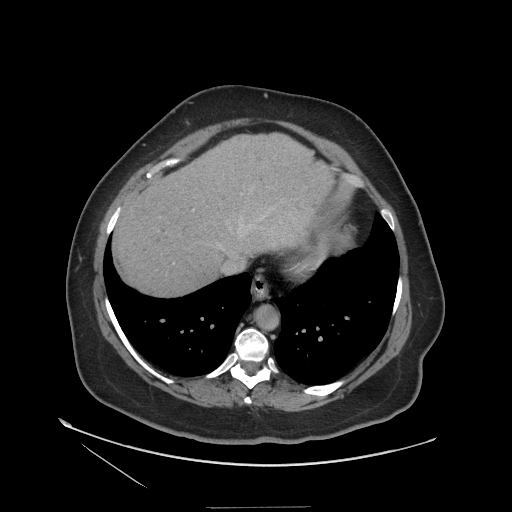
Contrast-enhanced abdominal CT (liver protocol), one axial slice; position 99 of 127 along the scan axis; 140 kVp; soft-tissue window (W 400 / L 40 HU); 2.5 mm slice thickness; 512 × 512 image matrix, field of view 480 × 480 mm. Case-level facts recorded for this patient, not image findings: diagnosis: hepatocellular carcinoma (patient treated with transarterial chemoembolisation; whether this scan precedes or follows treatment is not stated here); TNM stage (as recorded): Stage-II; Child-Pugh class: A; tumour differentiation: well differentiated.
Annotated regions visible in this slice (semi-automatically segmented with operator editing):
- liver parenchyma outside the tumour (the mass and vessels are separate outlines, so this box may not span the whole liver): bounding box [x1, y1, x2, y2] px = [112, 134, 333, 294]
- liver vessels: [240, 224, 250, 227]